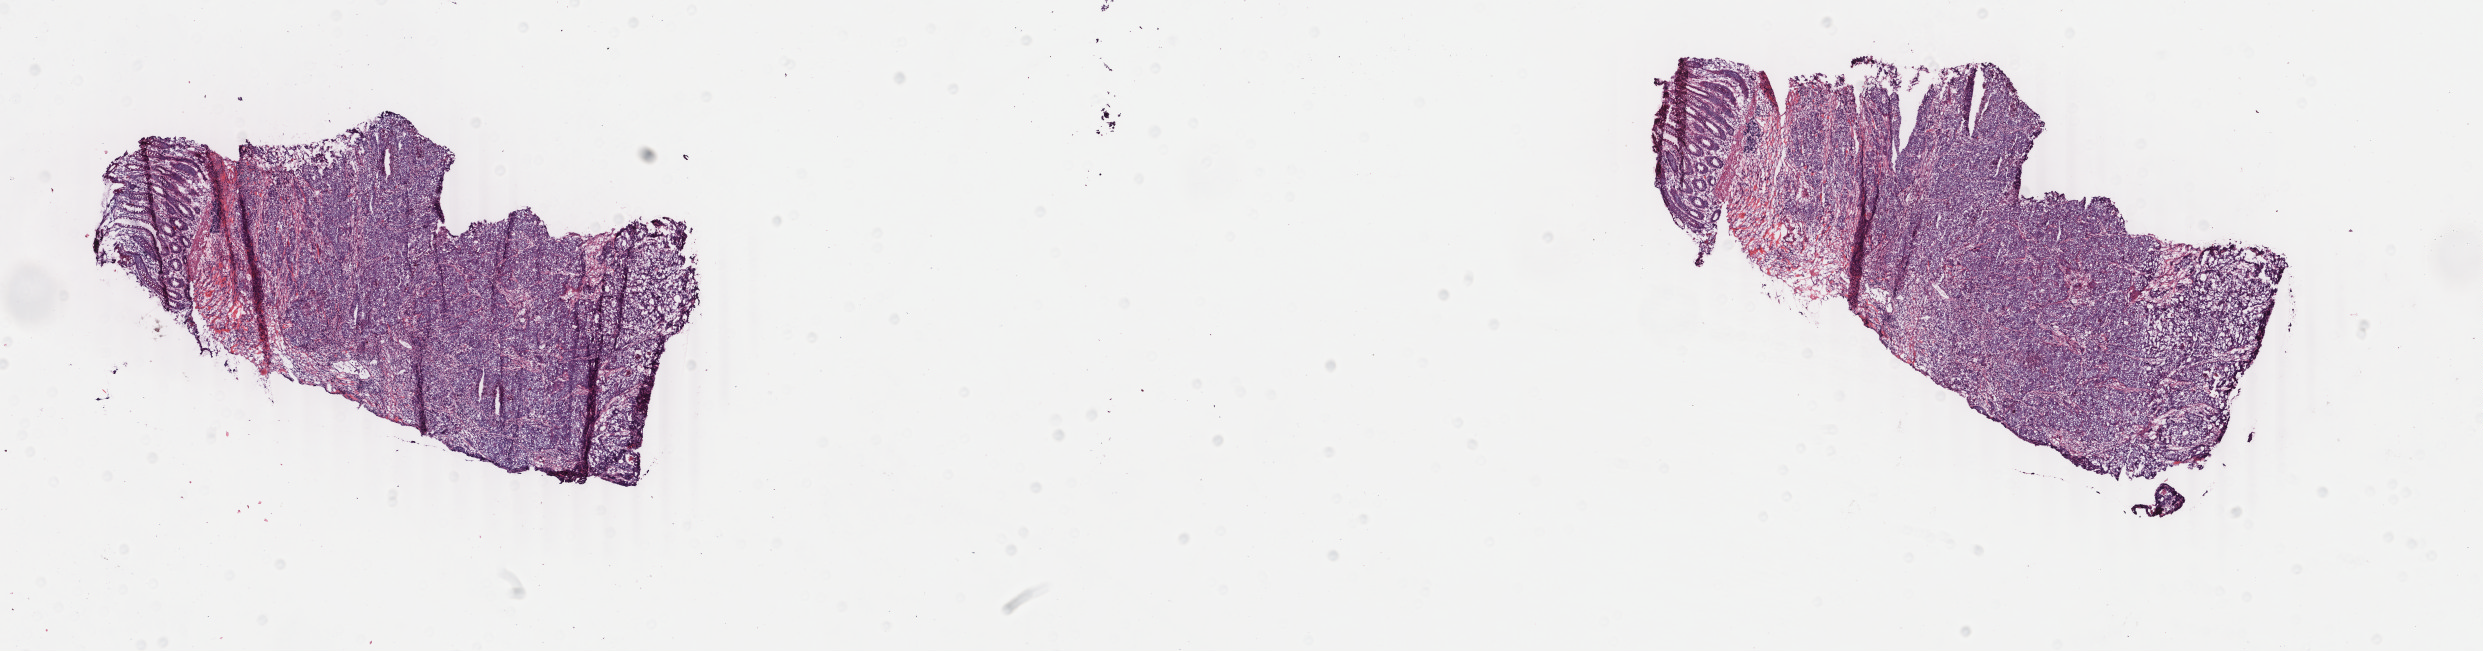
H&E whole-slide image — a low-resolution overview of the entire scanned area, about 19.8 x 5.2 mm, frozen section from the bottom of the tissue portion, sample: primary tumour, colon. Male, age 50 years at initial diagnosis. Composition of this section per pathologist review: tumour cells 77%, tumour nuclei 70%, normal cells 15%, stromal cells 5%, necrosis 3%. Infiltration values recorded for this section: lymphocyte infiltration 2%, monocyte infiltration 0%, neutrophil infiltration 10%.
* diagnosis: Adenocarcinoma, NOS (ascending colon)
* AJCC pathologic stage: IV
* TNM: T4 N2 M1
* lymph nodes positive (case pathology): 7 of 20 examined